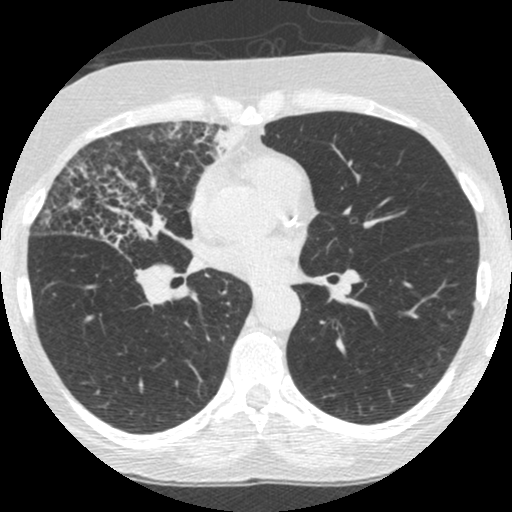
Low-dose screening chest CT, one axial slice; position 133 of 253 along the scan axis; 120 kVp; lung window (W 1500 / L -600 HU); 1.25 mm slice thickness; 512 × 512 image matrix, field of view 294 × 294 mm.
Outlined on this slice (outlined manually by an expert reader):
- lesion 4 (tumor, upper lobe of right lung): bounding box (x1, y1, x2, y2) in pixels: (206, 125, 252, 161)